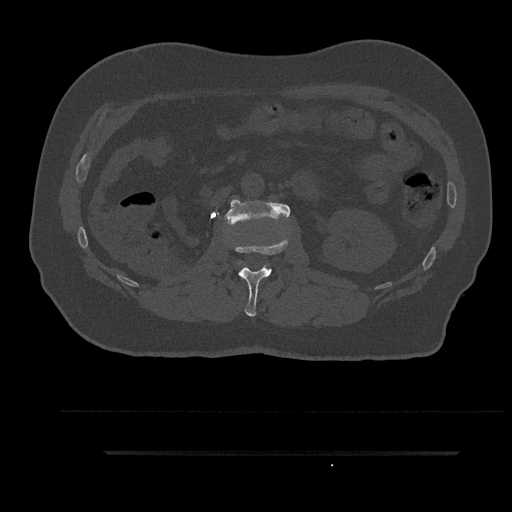
CT including the spine, one axial slice. Position 151 of 797 along the scan axis. Reconstruction kernel Br40s/3. Bone window (W 1800 / L 400 HU). 0.5 mm slice thickness. 512 × 512 image matrix, field of view 432 × 432 mm. Patient: male, 63 years. From the clinical record (not read from this slice): primary cancer: renal; vertebrae with lytic lesions (as recorded): T8.
Annotated regions visible in this slice (semi-automatic segmentation, software-assisted and operator-edited):
- L1 vertebra: bounding box <233,238,289,317> (left, top, right, bottom; pixels)
- L2 vertebra: <224,199,291,226>